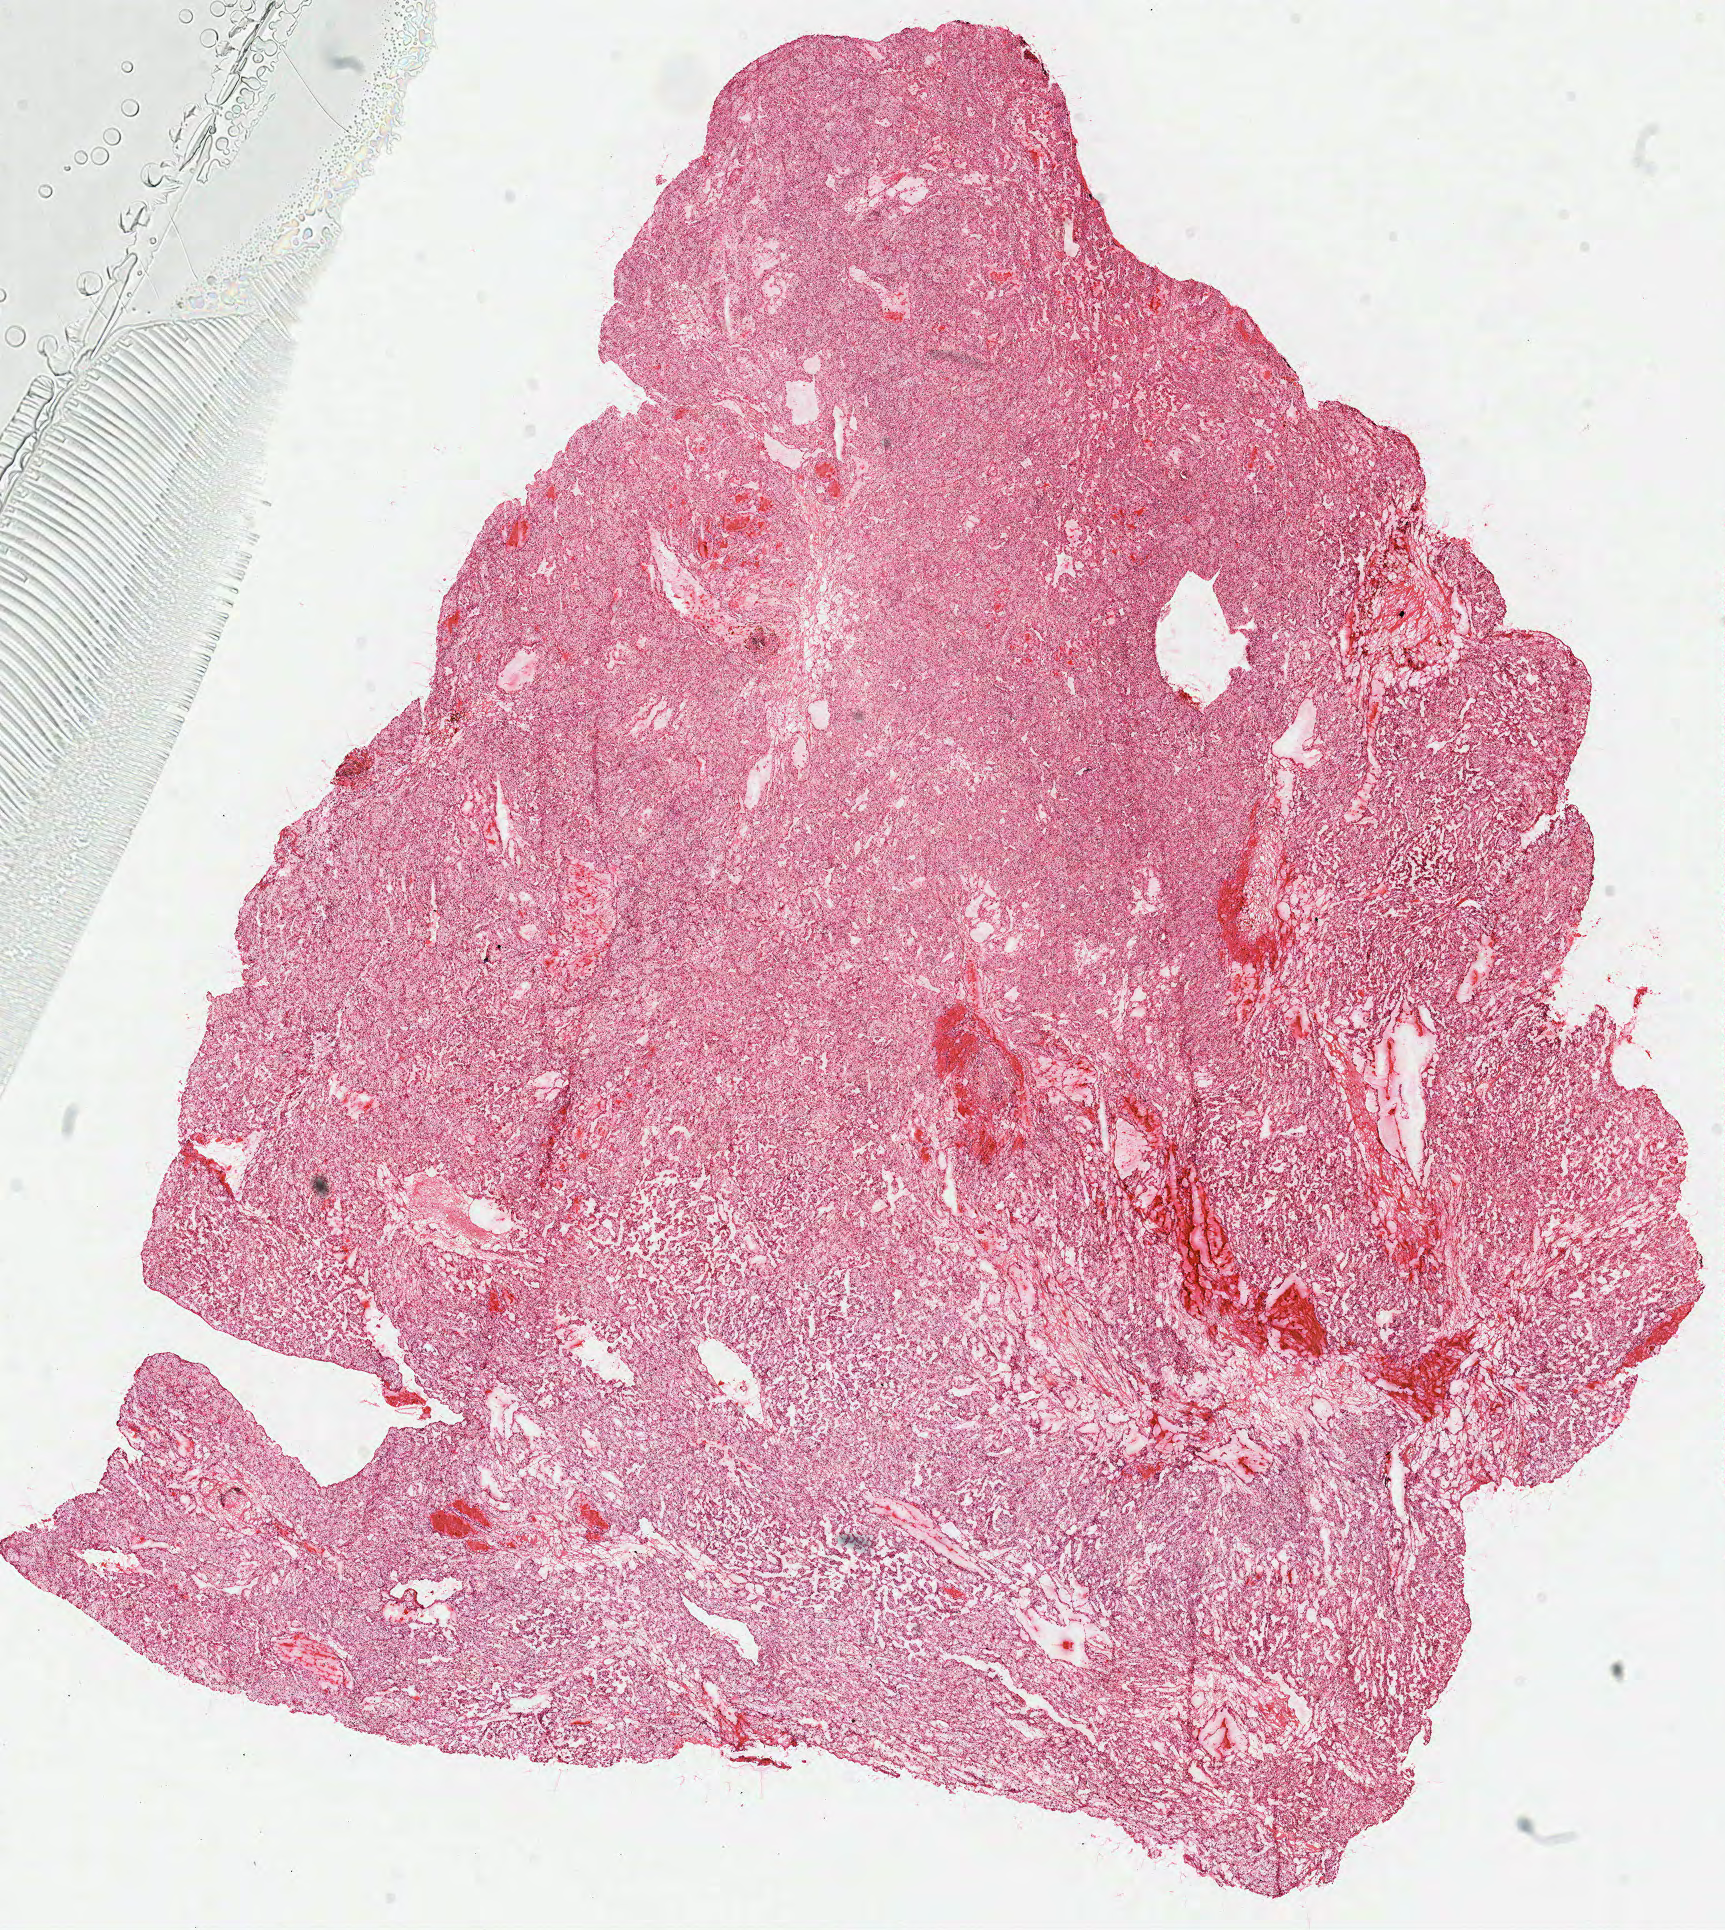
Hematoxylin and eosin (H&E) stained whole-slide image — a low-resolution overview of the entire scanned area, about 13.6 x 15.2 mm, frozen section from the top of the tissue portion, sample: primary tumour, kidney. Male patient; age at initial diagnosis 61 years. Pathologist review of this section (percent, as recorded): tumour cells 95%, tumour nuclei 85%.
Diagnosis: Clear cell adenocarcinoma, NOS.